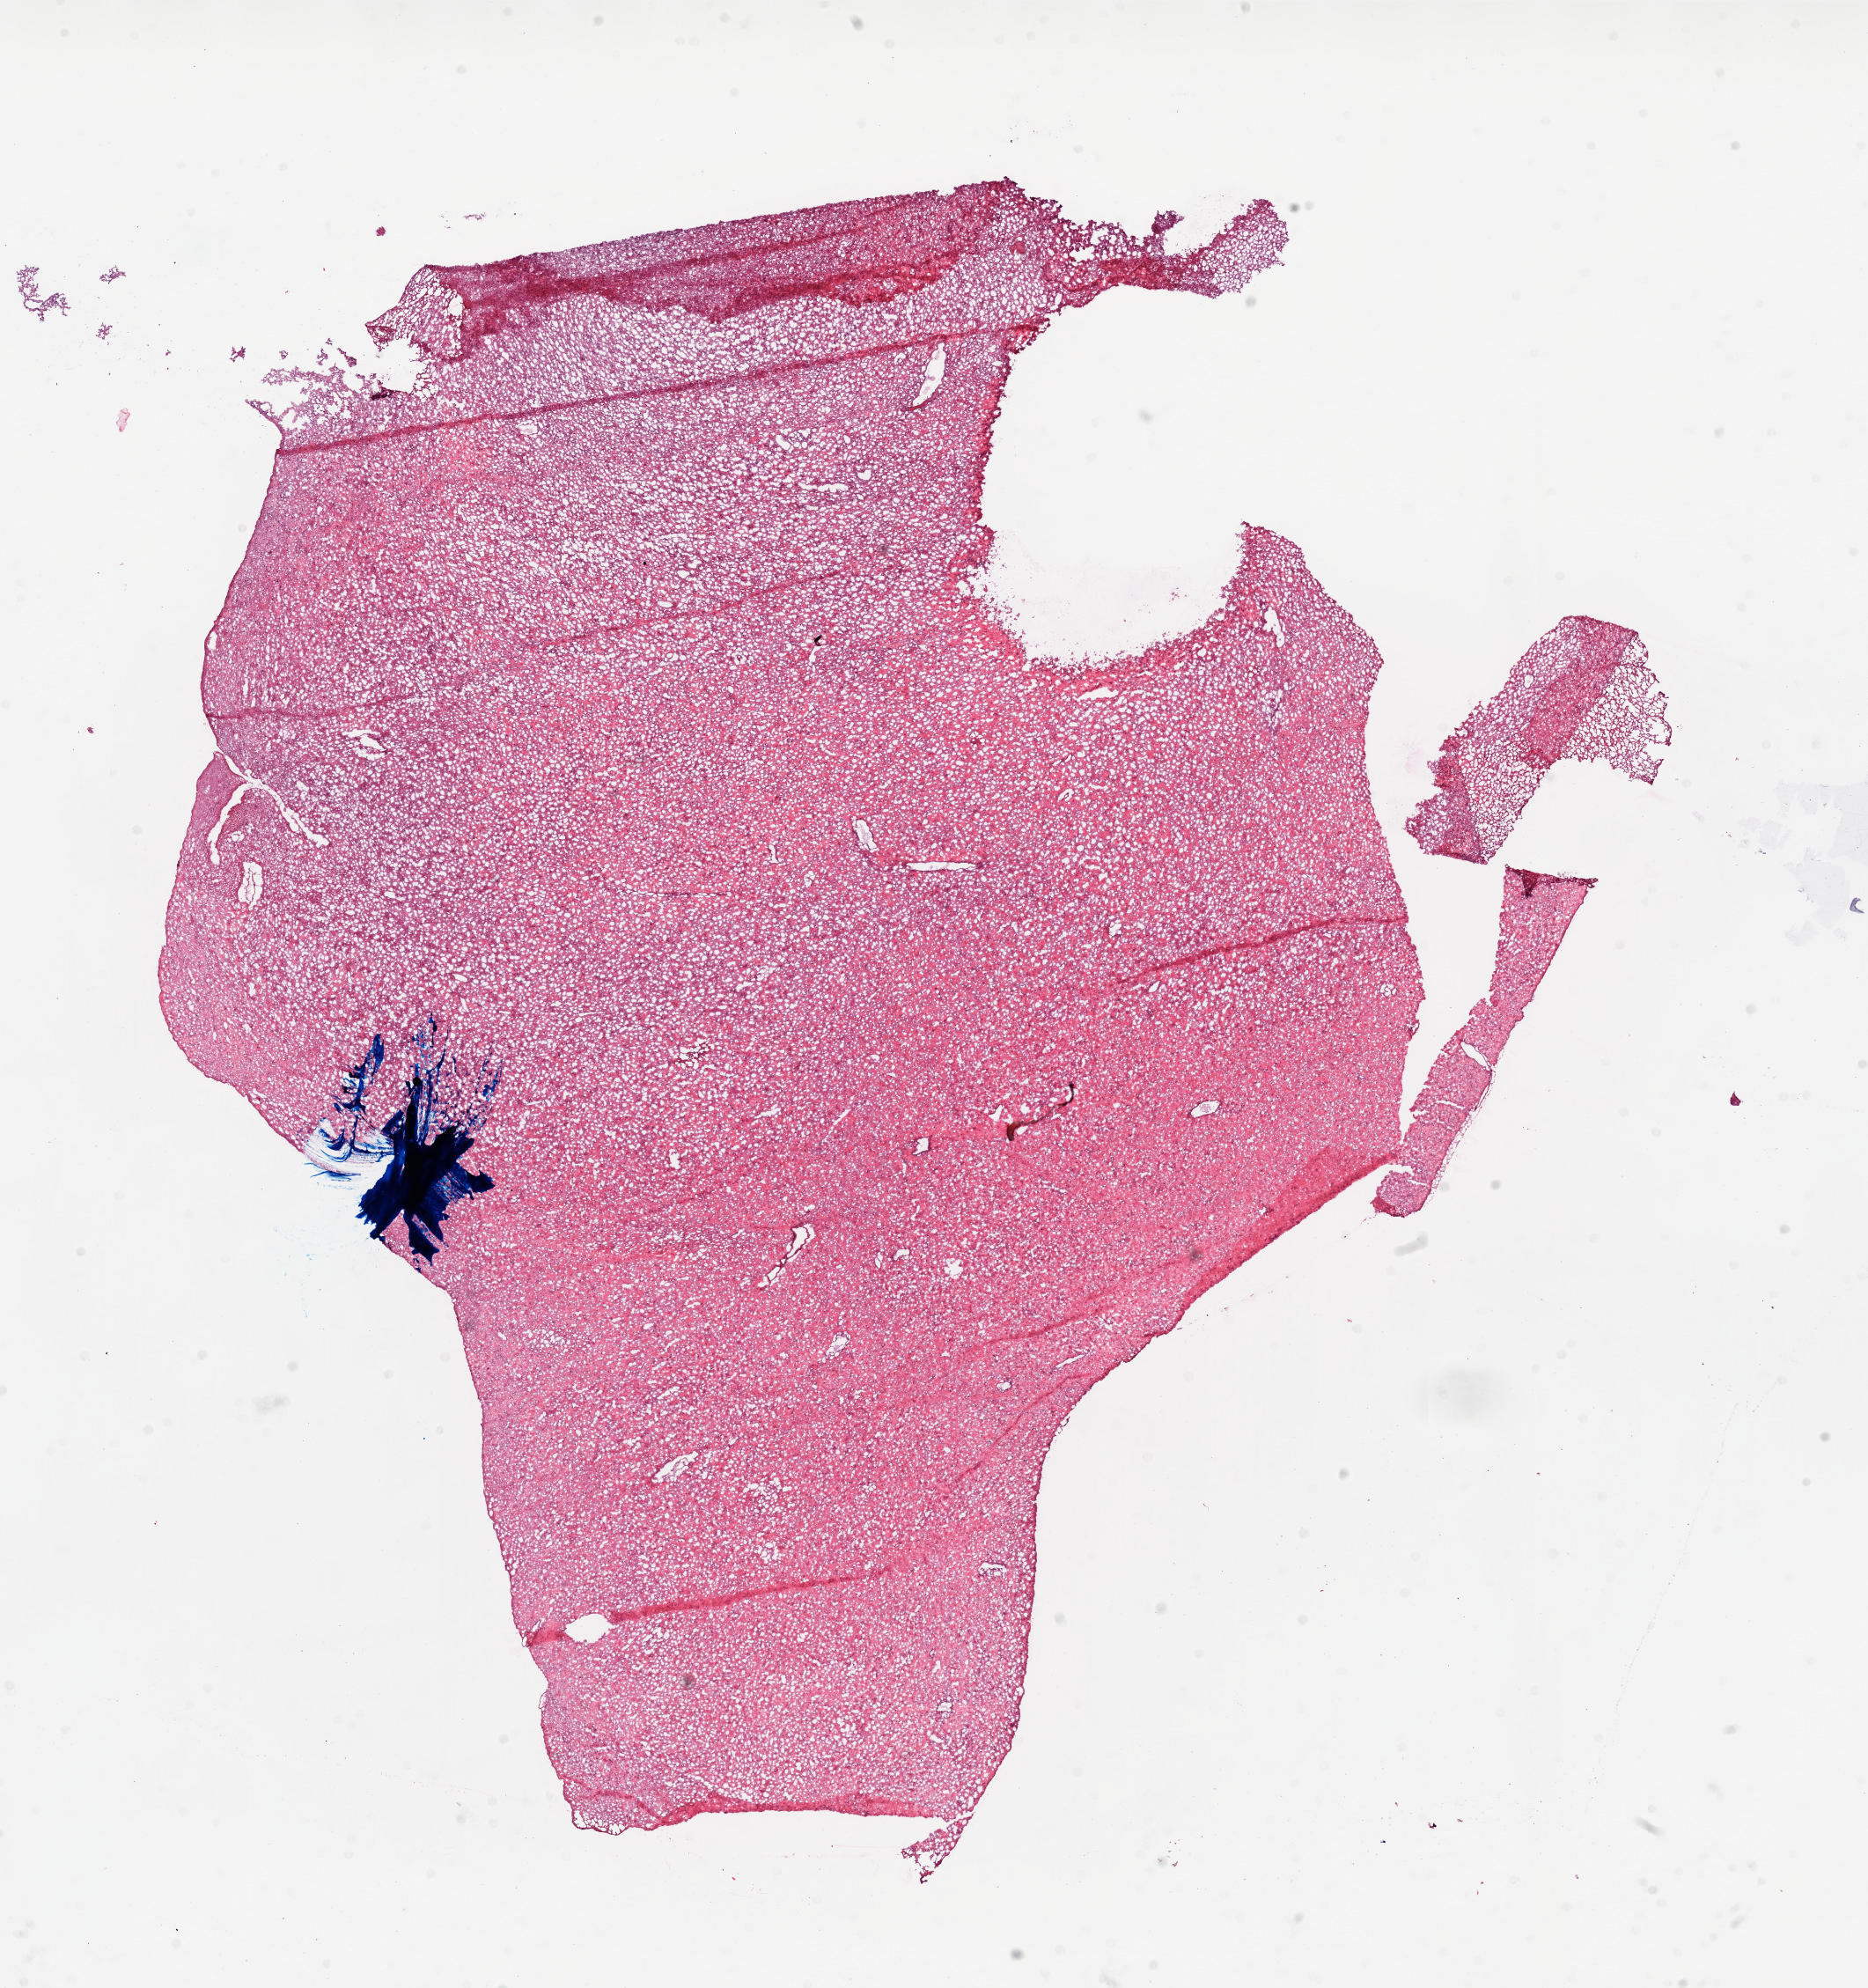
H&E whole-slide image, low-resolution overview of the scanned area, about 17.0 x 18.1 mm. Composition of this section per pathologist review: tumour cells 20%, tumour nuclei 100%, stromal cells 80%, necrosis 0%.
Specimen: frozen section from the top of the tissue portion; brain, primary tumour sample.